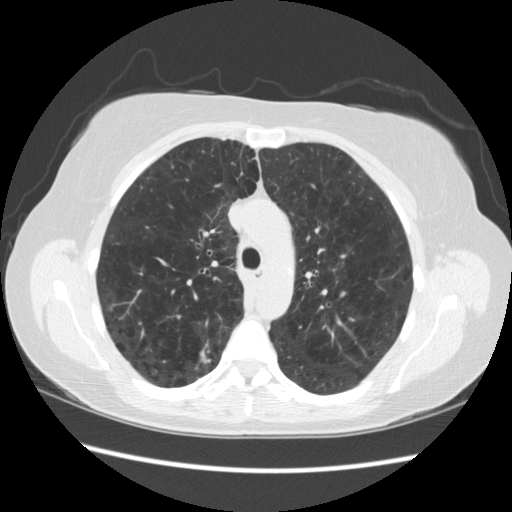
Low-dose screening chest CT, one axial slice; position 166 of 235 along the scan axis; reconstruction kernel STANDARD; lung window (W 1500 / L -600 HU); 512 × 512 image matrix.
Outlined on this slice (outlined manually by an expert reader):
- lesion 1 (tumor, upper lobe of right lung): bounding box [x1, y1, x2, y2] px = [198, 348, 213, 364]